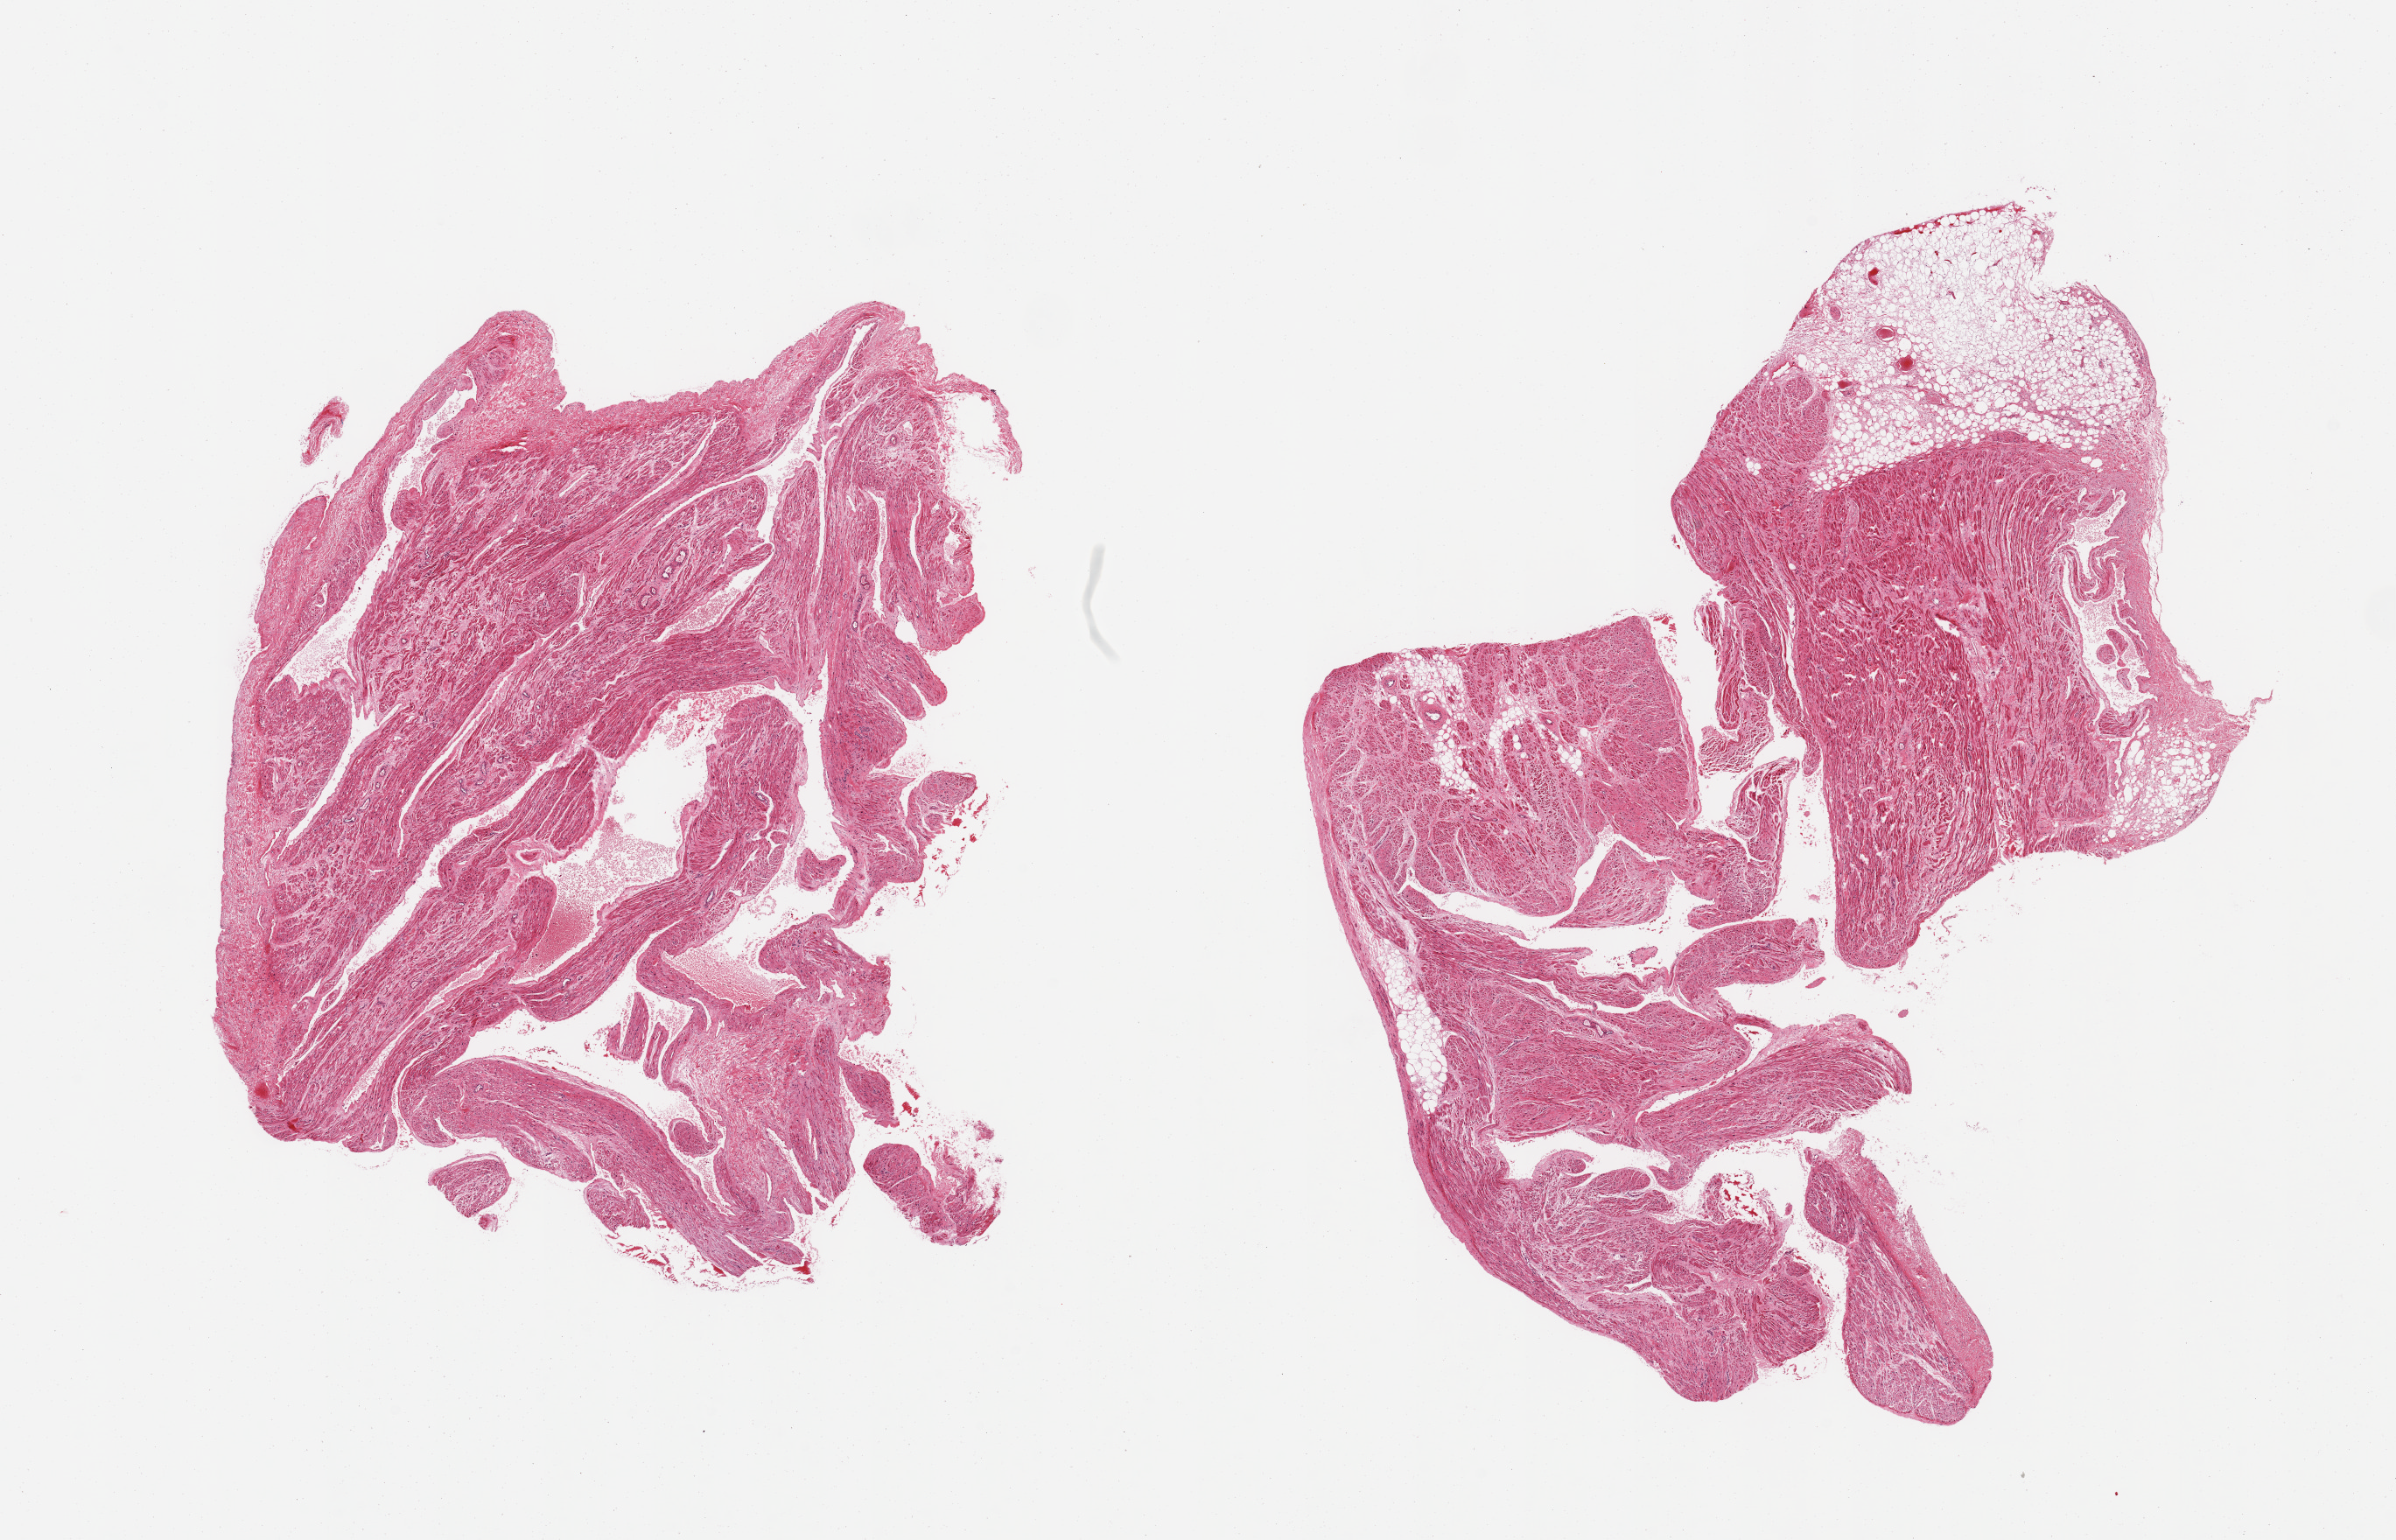
H&E whole-slide image, a low-resolution overview of the entire scanned area, about 21.7 x 13.9 mm (acquisition: 20x scan). PAXgene-fixed, paraffin-embedded tissue. Section of auricular appendage (target tissue). Donor tissue sample. Donor: male.
Reviewer comment on this tissue sample: 2 pieces, no abnormalities.